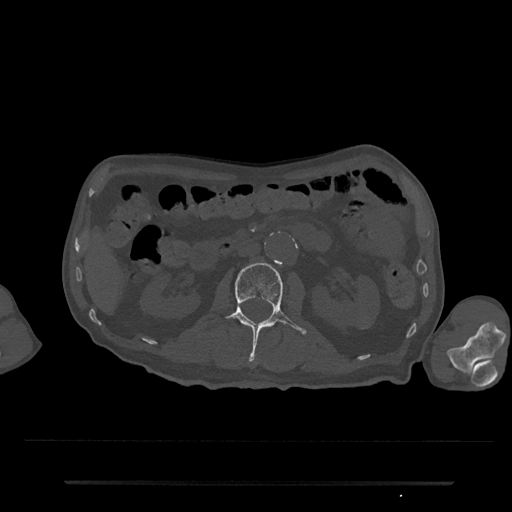
CT including the spine, one axial slice; reconstruction kernel Br40s/3; 120 kVp; bone window (W 1800 / L 400 HU); 512 × 512 image matrix. Male patient, age 74 years. Case-level facts recorded for this patient, not image findings: primary cancer: prostate.
Structures marked on this image (semi-automatically segmented with operator editing):
- L2 vertebra: bounding box <225,263,307,361> (left, top, right, bottom; pixels)